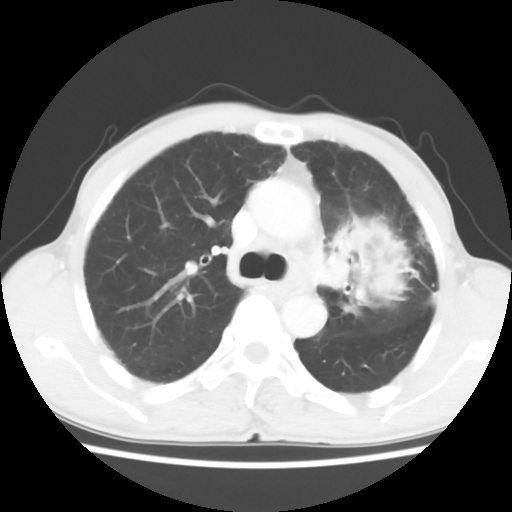
Chest CT, one axial slice; slice 40 of 60 in the series (ordered by position); reconstruction kernel STANDARD; 120 kVp; lung window (W 1500 / L -600 HU); 5 mm slice thickness; 512 × 512 image matrix. Male patient, age 64 years. From the clinical record (not read from this slice): clinical TNM (as recorded): T3 N3 M0; histopathological grade: G3.
Annotated regions visible in this slice (rectangle marked by the reading radiologist):
- lung tumour (recorded histology: adenocarcinoma): bounding box [x1, y1, x2, y2] px = [329, 200, 423, 331]